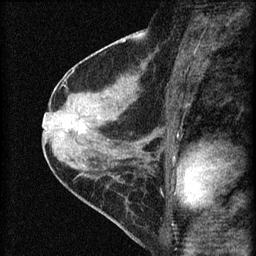
Breast MRI (dynamic contrast-enhanced), one sagittal slice; slice 32 of 60 in the series (ordered by position); dynamic contrast-enhanced series, image 2 of 4 at this slice position (ordered by acquisition); 1.5 T; TE 4.2 ms, TR 8.2 ms; 2 mm slice thickness; 256 × 256 image matrix, field of view 180 × 180 mm. Female patient, age 45 years.
Structures marked on this image (semi-automatic segmentation, software-assisted and operator-edited):
- analysis volume of interest (the breast-tissue region the enhancement analysis was run in; not a lesion): bounding box (x1, y1, x2, y2) in pixels: (58, 107, 98, 147)
- tumour enhancement mask (voxels above the 70 % enhancement threshold inside the analysis volume of interest): (63, 116, 71, 127)